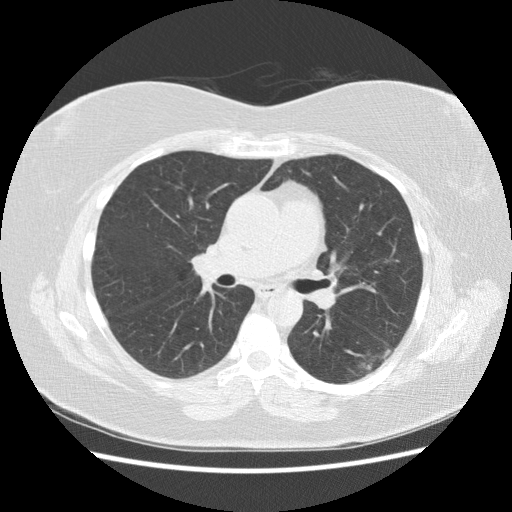
Chest CT (low-dose screening protocol), one axial image. Third screening round (two years after baseline). Lung window (W 1500 / L -600 HU). 512 × 512 image matrix. Female, age 57 years at enrolment.
Lesion marked by an expert reader, box from (x=329, y=325) to (x=414, y=387) px. Reader record for this screening exam (exam-level; its link to the box is not recorded): non-calcified nodule or mass ≥4 mm, left lower lobe, 40 × 20 mm, poorly defined margins, mixed attenuation, pre-existing on the prior screen: yes; interval growth: yes. Participant outcome: lung cancer diagnosed 55 days after this screen — squamous cell carcinoma, NOS, left lower lobe, poorly differentiated (G3), stage IB (AJCC 6th edition), 40 mm at pathology.